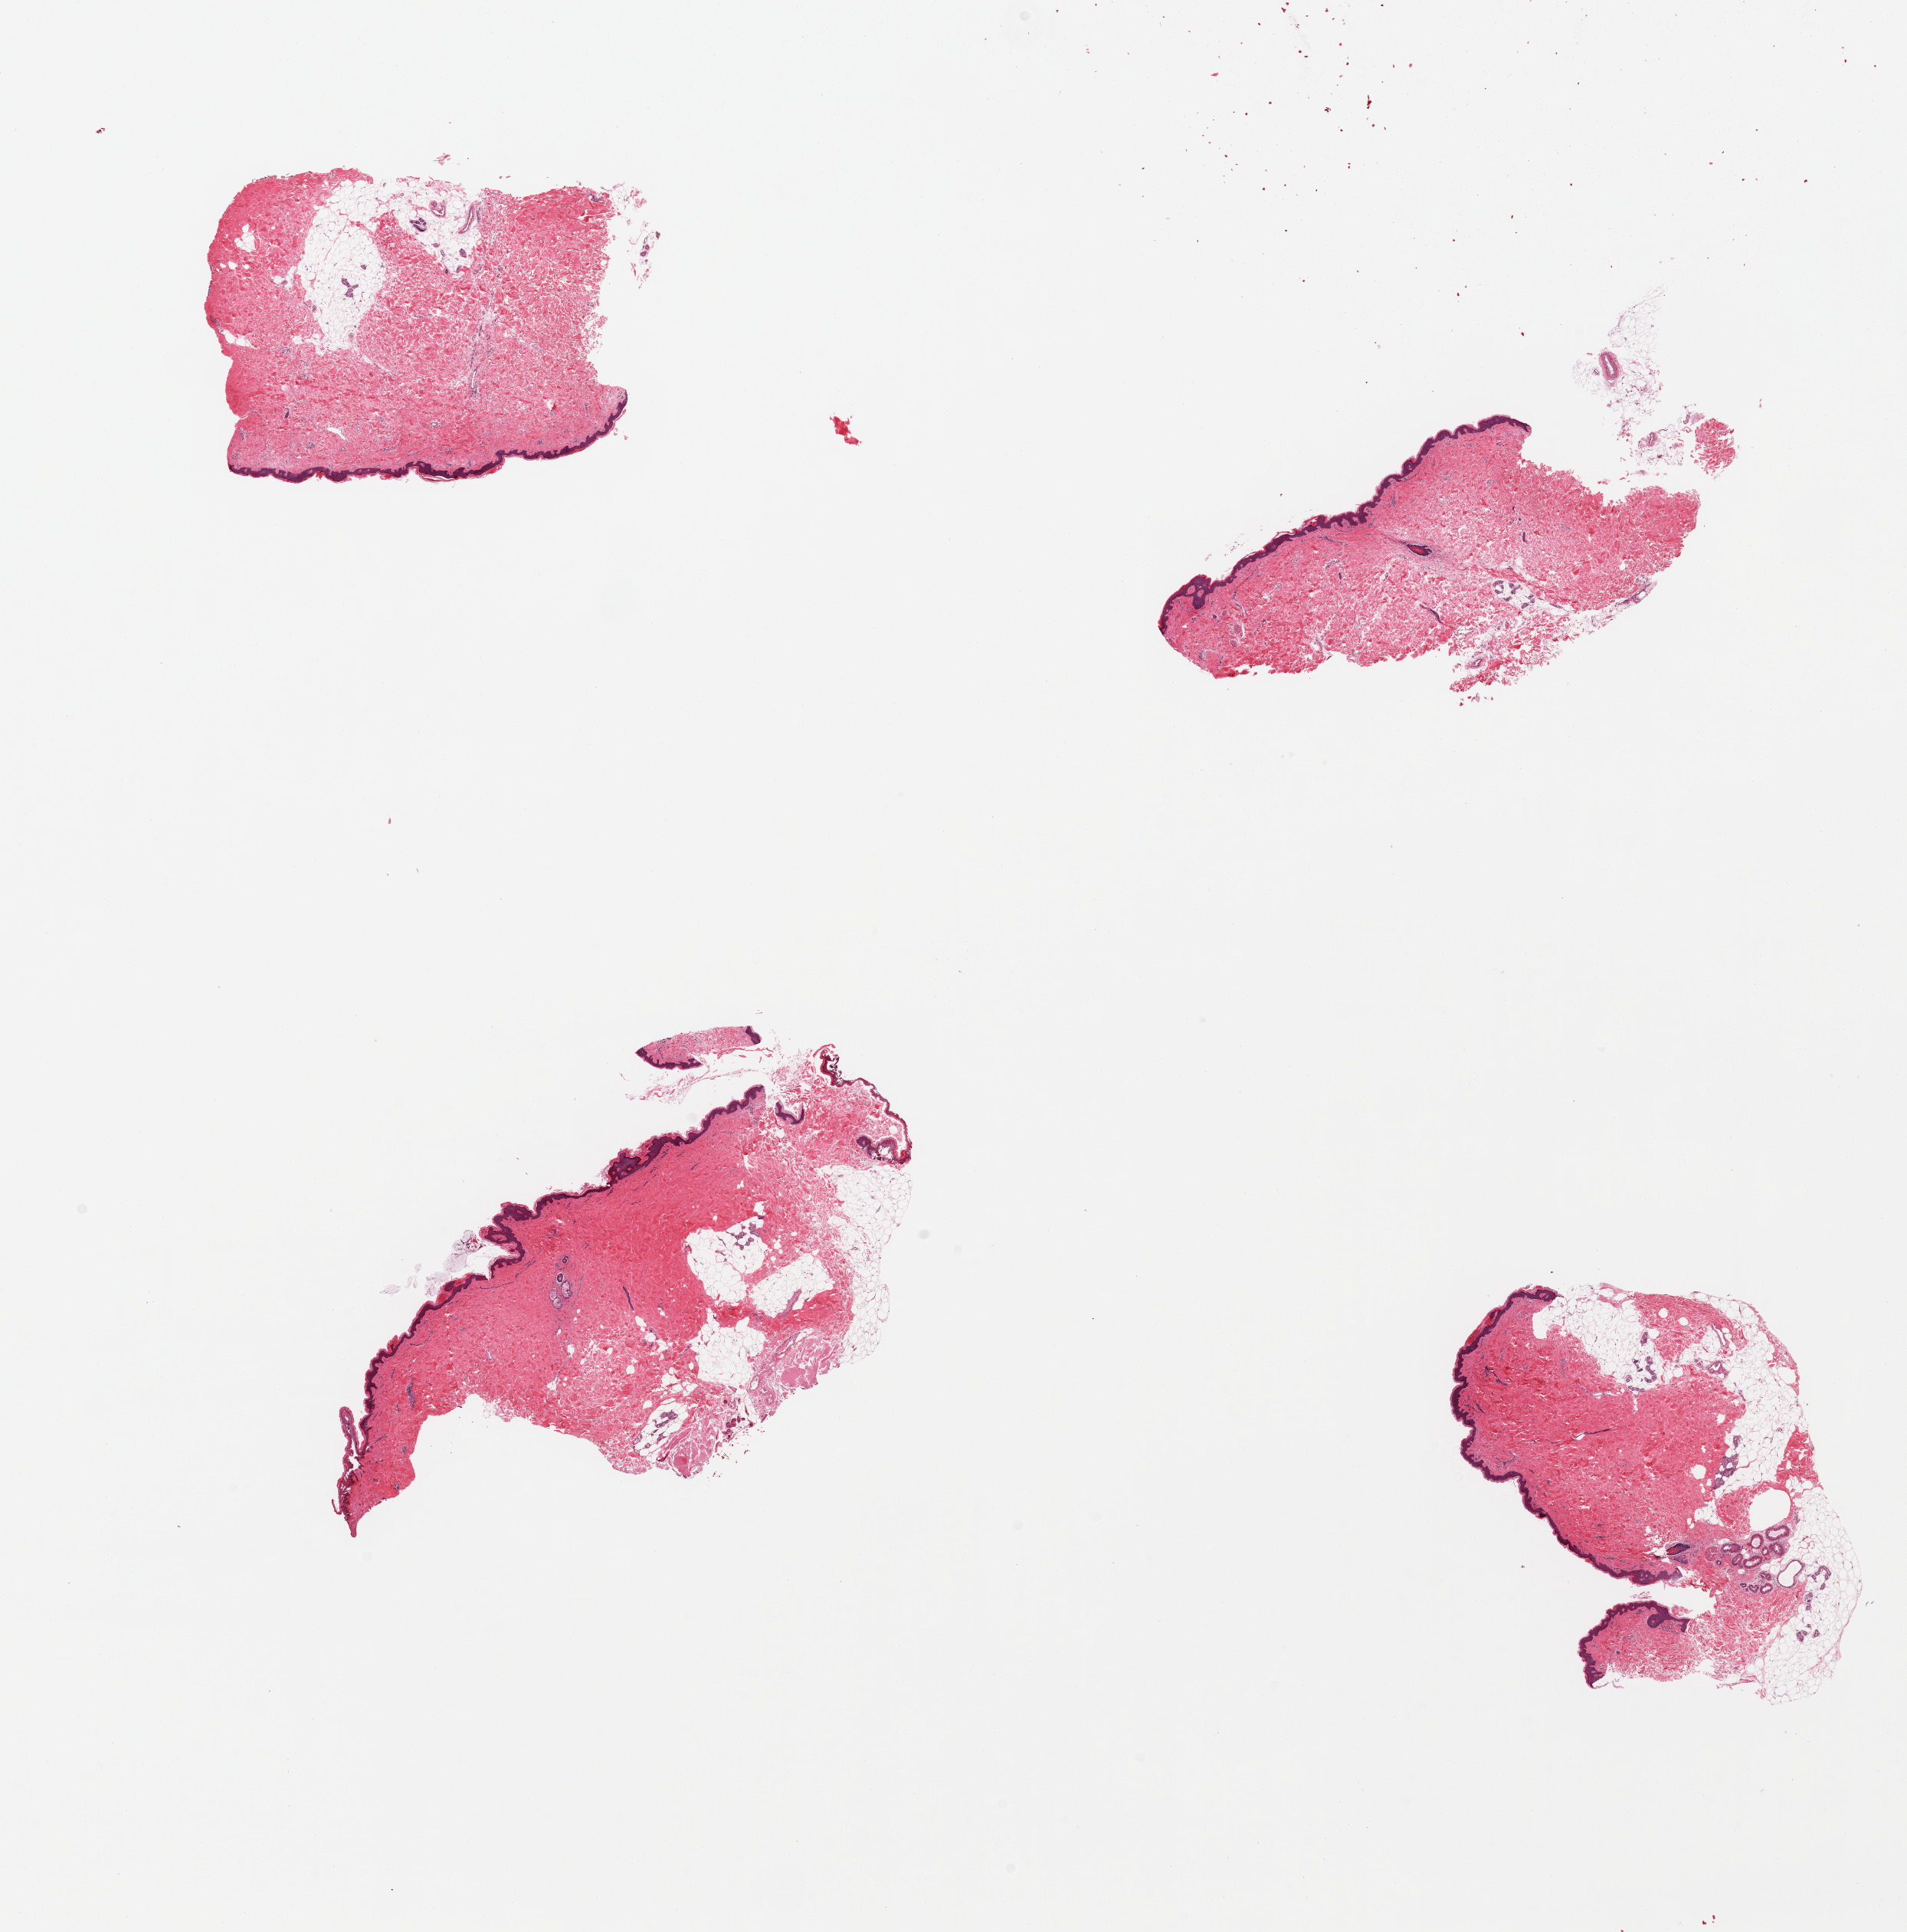
Digitized H&E-stained section — shown as a low-resolution overview of the whole scanned area (about 19.7 x 19.9 mm, from a 20x scan). PAXgene-fixed, paraffin-embedded tissue. Target tissue: skin of suprapubic region. Tissue donor sample. Donor sex: female.
• reviewer comment on this tissue sample: 4 pieces. Squamous epithelium is ~50-60 microns thick